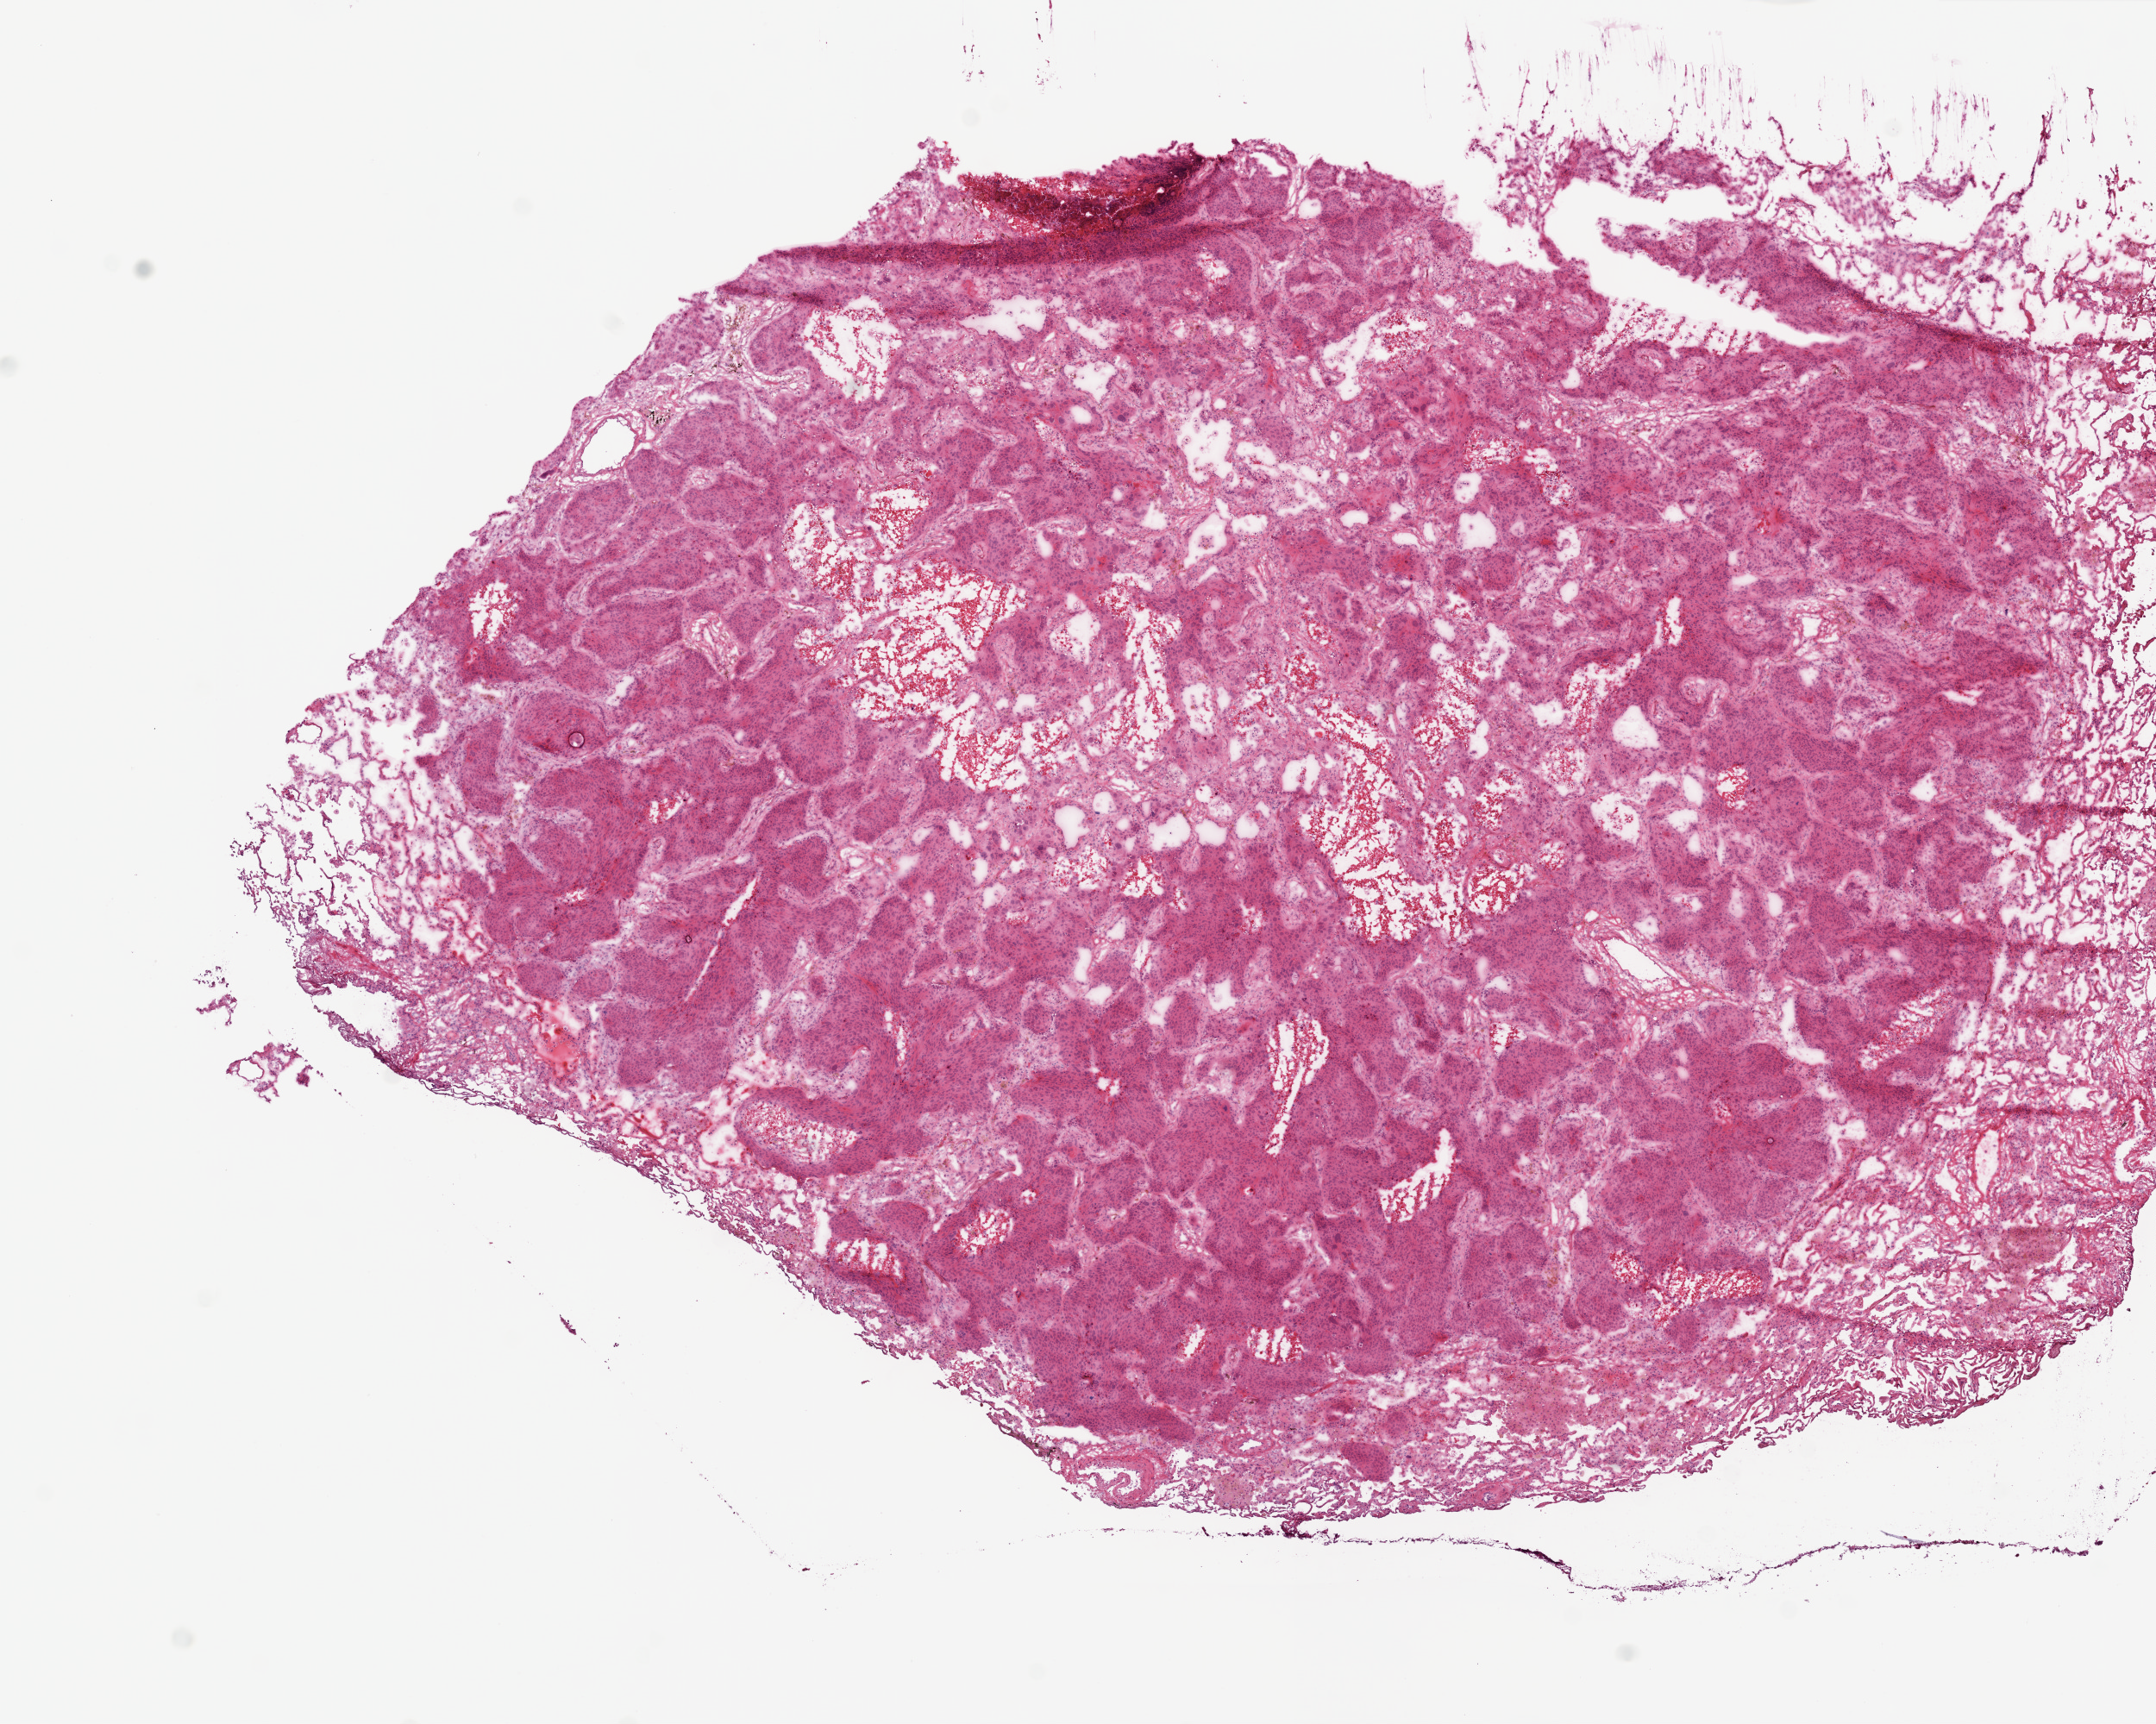
Digitized H&E-stained tissue section (whole slide) — shown as a low-resolution overview of the whole scanned area (about 10.0 x 8.0 mm); frozen section; sample: primary tumour, lung. Patient: female, age at initial diagnosis 58 years. Slide review estimates, as recorded: tumour cells 76%, tumour nuclei 80%, normal cells 18%, stromal cells 0%, necrosis 6%. Infiltration values recorded for this section: lymphocyte infiltration 5%, monocyte infiltration 1%, neutrophil infiltration 1%.
Histologic diagnosis: Squamous cell carcinoma, NOS (upper lobe, lung). Laterality: right. AJCC pathologic stage: IA.